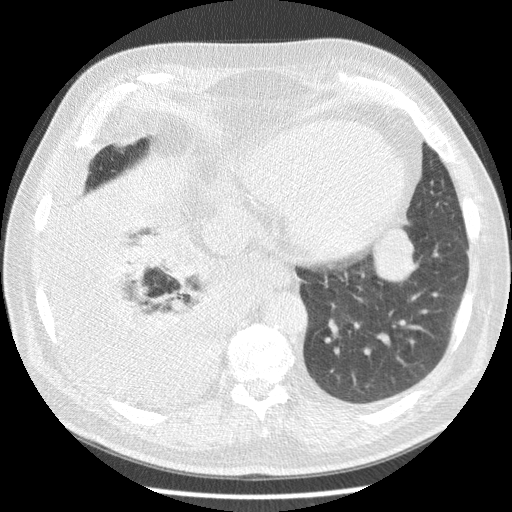
Low-dose screening chest CT, one axial slice; position 59 of 180 along the scan axis; 120 kVp; lung window (W 1500 / L -600 HU); 2.5 mm slice thickness; 512 × 512 image matrix.
Annotated regions visible in this slice (manually delineated by an expert):
- lesion 1 (tumor, lower lobe of left lung): box from (x=373, y=229) to (x=418, y=282) px